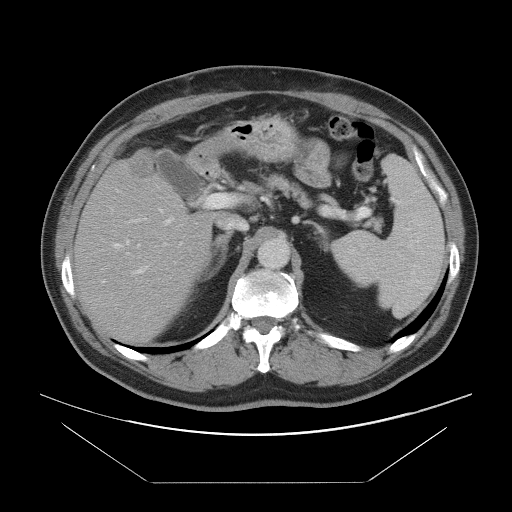
Contrast-enhanced abdominal CT, one axial slice. Slice 56 of 97 in the series (ordered by position). 120 kVp. Intravenous contrast given. Soft-tissue window (W 400 / L 40 HU). 512 × 512 image matrix. Male patient, age 62 years. Case-level facts recorded for this patient, not image findings: diagnosis: colorectal cancer liver metastases, imaged before liver resection; multiple liver metastases: no; largest metastasis: 7 cm; disease in both lobes: yes.
Annotated regions visible in this slice (outlined manually by an expert reader):
- hepatic veins: bounding box [x1, y1, x2, y2] px = [114, 184, 167, 255]
- liver: [76, 151, 215, 343]
- planned liver remnant (the part of the liver to remain after resection): [75, 176, 215, 343]
- portal vein (with intrahepatic branches): [124, 194, 228, 272]
- liver metastasis: [130, 151, 154, 180]